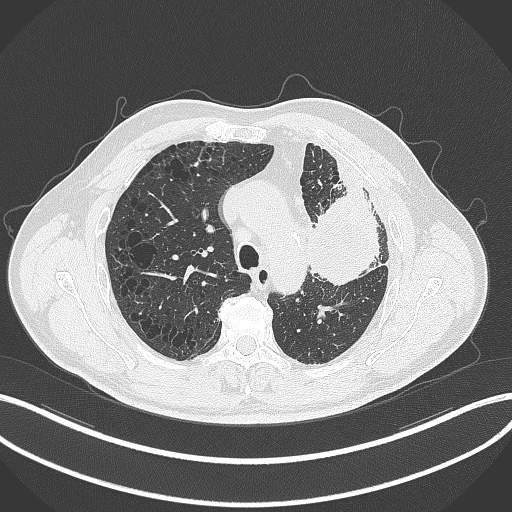
Chest CT, one axial slice; slice 223 of 297 in the series (ordered by position); reconstruction kernel B70f; 120 kVp; lung window (W 1500 / L -600 HU); 1 mm slice thickness; 512 × 512 image matrix. Male patient, age 68 years. From the clinical record (not read from this slice): clinical TNM (as recorded): T3 N3 M1.
Annotated regions visible in this slice (rectangle marked by the reading radiologist):
- lung tumour (recorded histology: adenocarcinoma): bounding box [x1, y1, x2, y2] px = [306, 179, 389, 291]